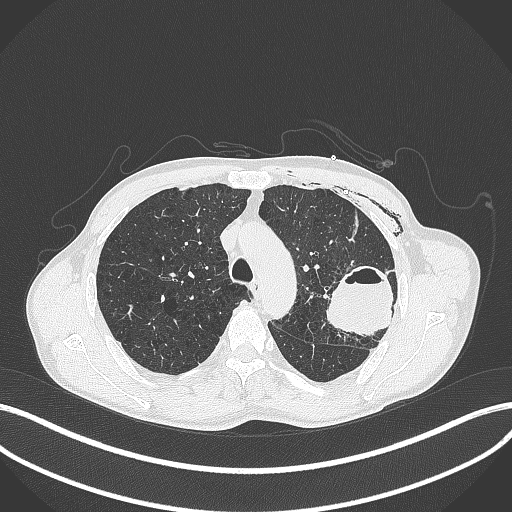
Chest CT, one axial slice; position 297 of 457 along the scan axis; reconstruction kernel B70f; 120 kVp; lung window (W 1500 / L -600 HU); 1 mm slice thickness; 512 × 512 image matrix, field of view 400 × 400 mm. Male patient, age 58 years. Case-level facts recorded for this patient, not image findings: clinical TNM (as recorded): T3 N0 M0.
Annotated regions visible in this slice (bounding box drawn by a radiologist):
- lung tumour (recorded histology: adenocarcinoma): bounding box [x1, y1, x2, y2] px = [325, 258, 398, 338]